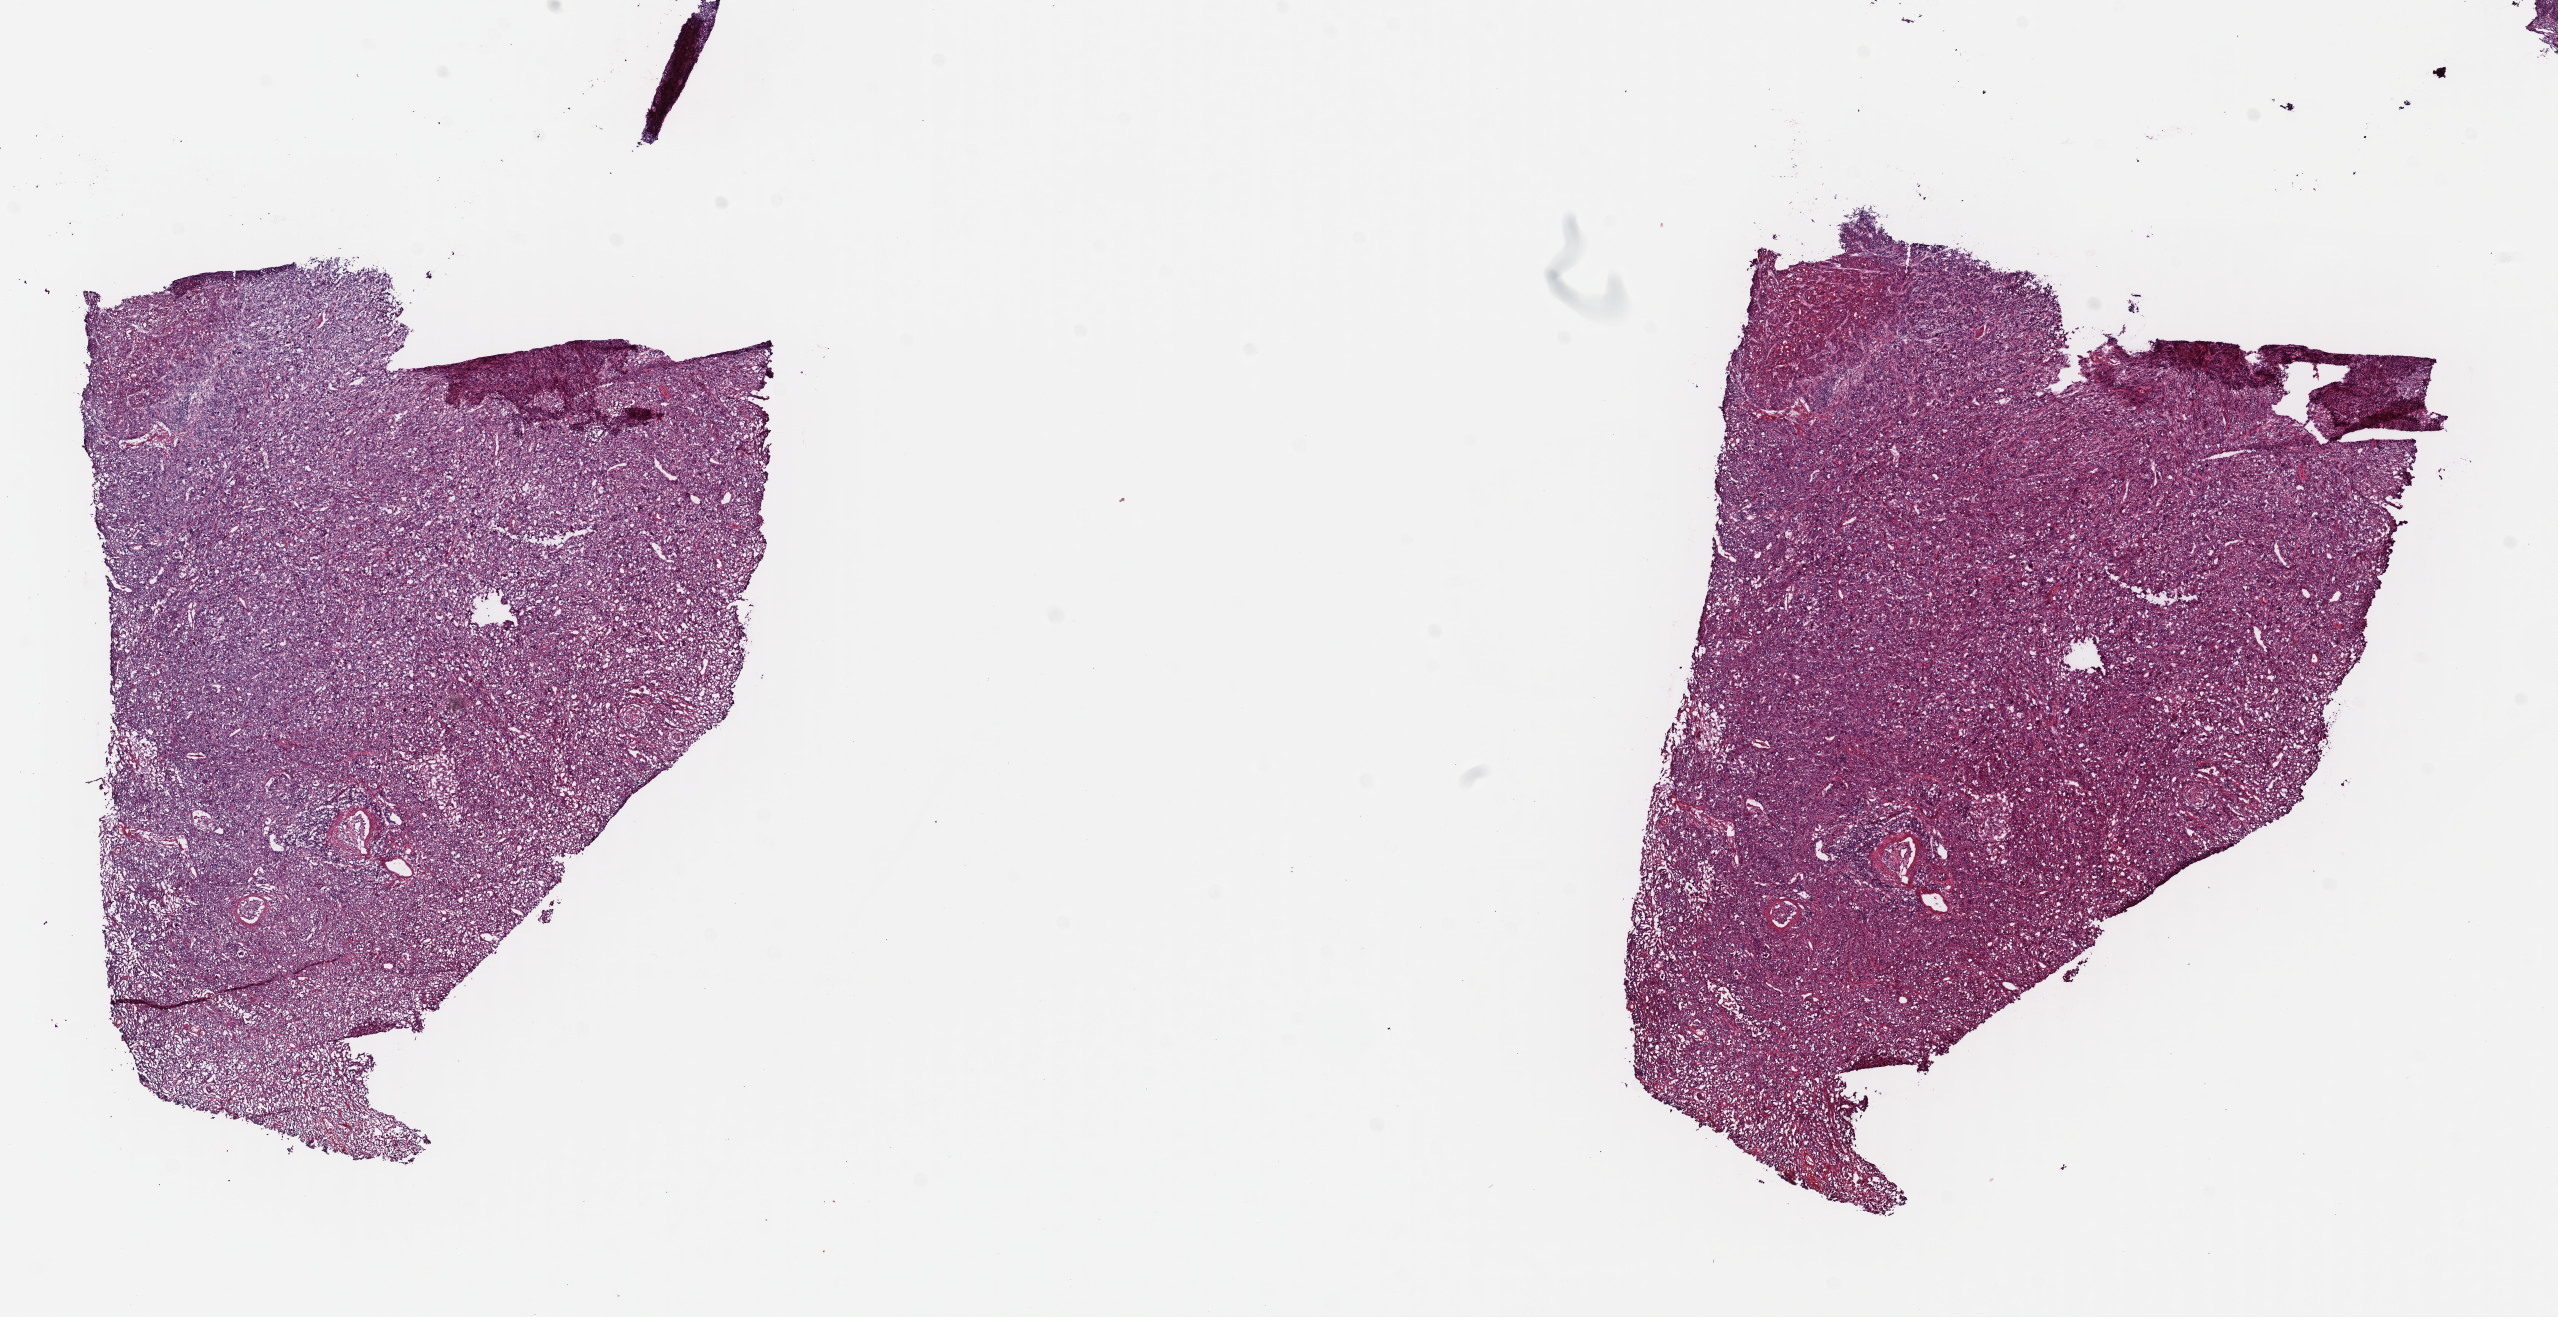
Digitized H&E tissue section (whole slide), shown as a low-resolution overview of the whole scanned area (about 20.1 x 10.4 mm, slide scanned at 40x), frozen section from the top of the tissue portion, sample: primary tumour, cervix. Patient: female, age at initial diagnosis 36 years. Histologic grade: G3 (poorly differentiated). Slide review estimates, as recorded: tumour cells 100%, tumour nuclei 85%, normal cells 0%, stromal cells 0%, necrosis 0%. Infiltration values recorded for this section: lymphocyte infiltration 0%, monocyte infiltration 0%, neutrophil infiltration 0%.
Diagnosis: Squamous cell carcinoma, NOS (cervix uteri). FIGO stage: IB.